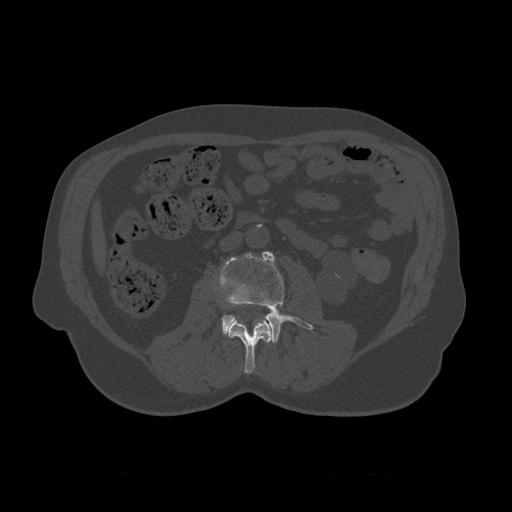
CT including the spine, one axial slice; slice 316 of 450 in the series (ordered by position); reconstruction kernel STANDARD; 120 kVp; bone window (W 1800 / L 400 HU); 1.25 mm slice thickness; 512 × 512 image matrix, field of view 405 × 405 mm. Patient age 75 years. From the clinical record (not read from this slice): primary cancer: prostate.
Outlined on this slice (semi-automatically segmented with operator editing):
- L2 vertebra: bounding box (x1, y1, x2, y2) in pixels: (228, 316, 274, 374)
- L3 vertebra: (217, 251, 314, 343)